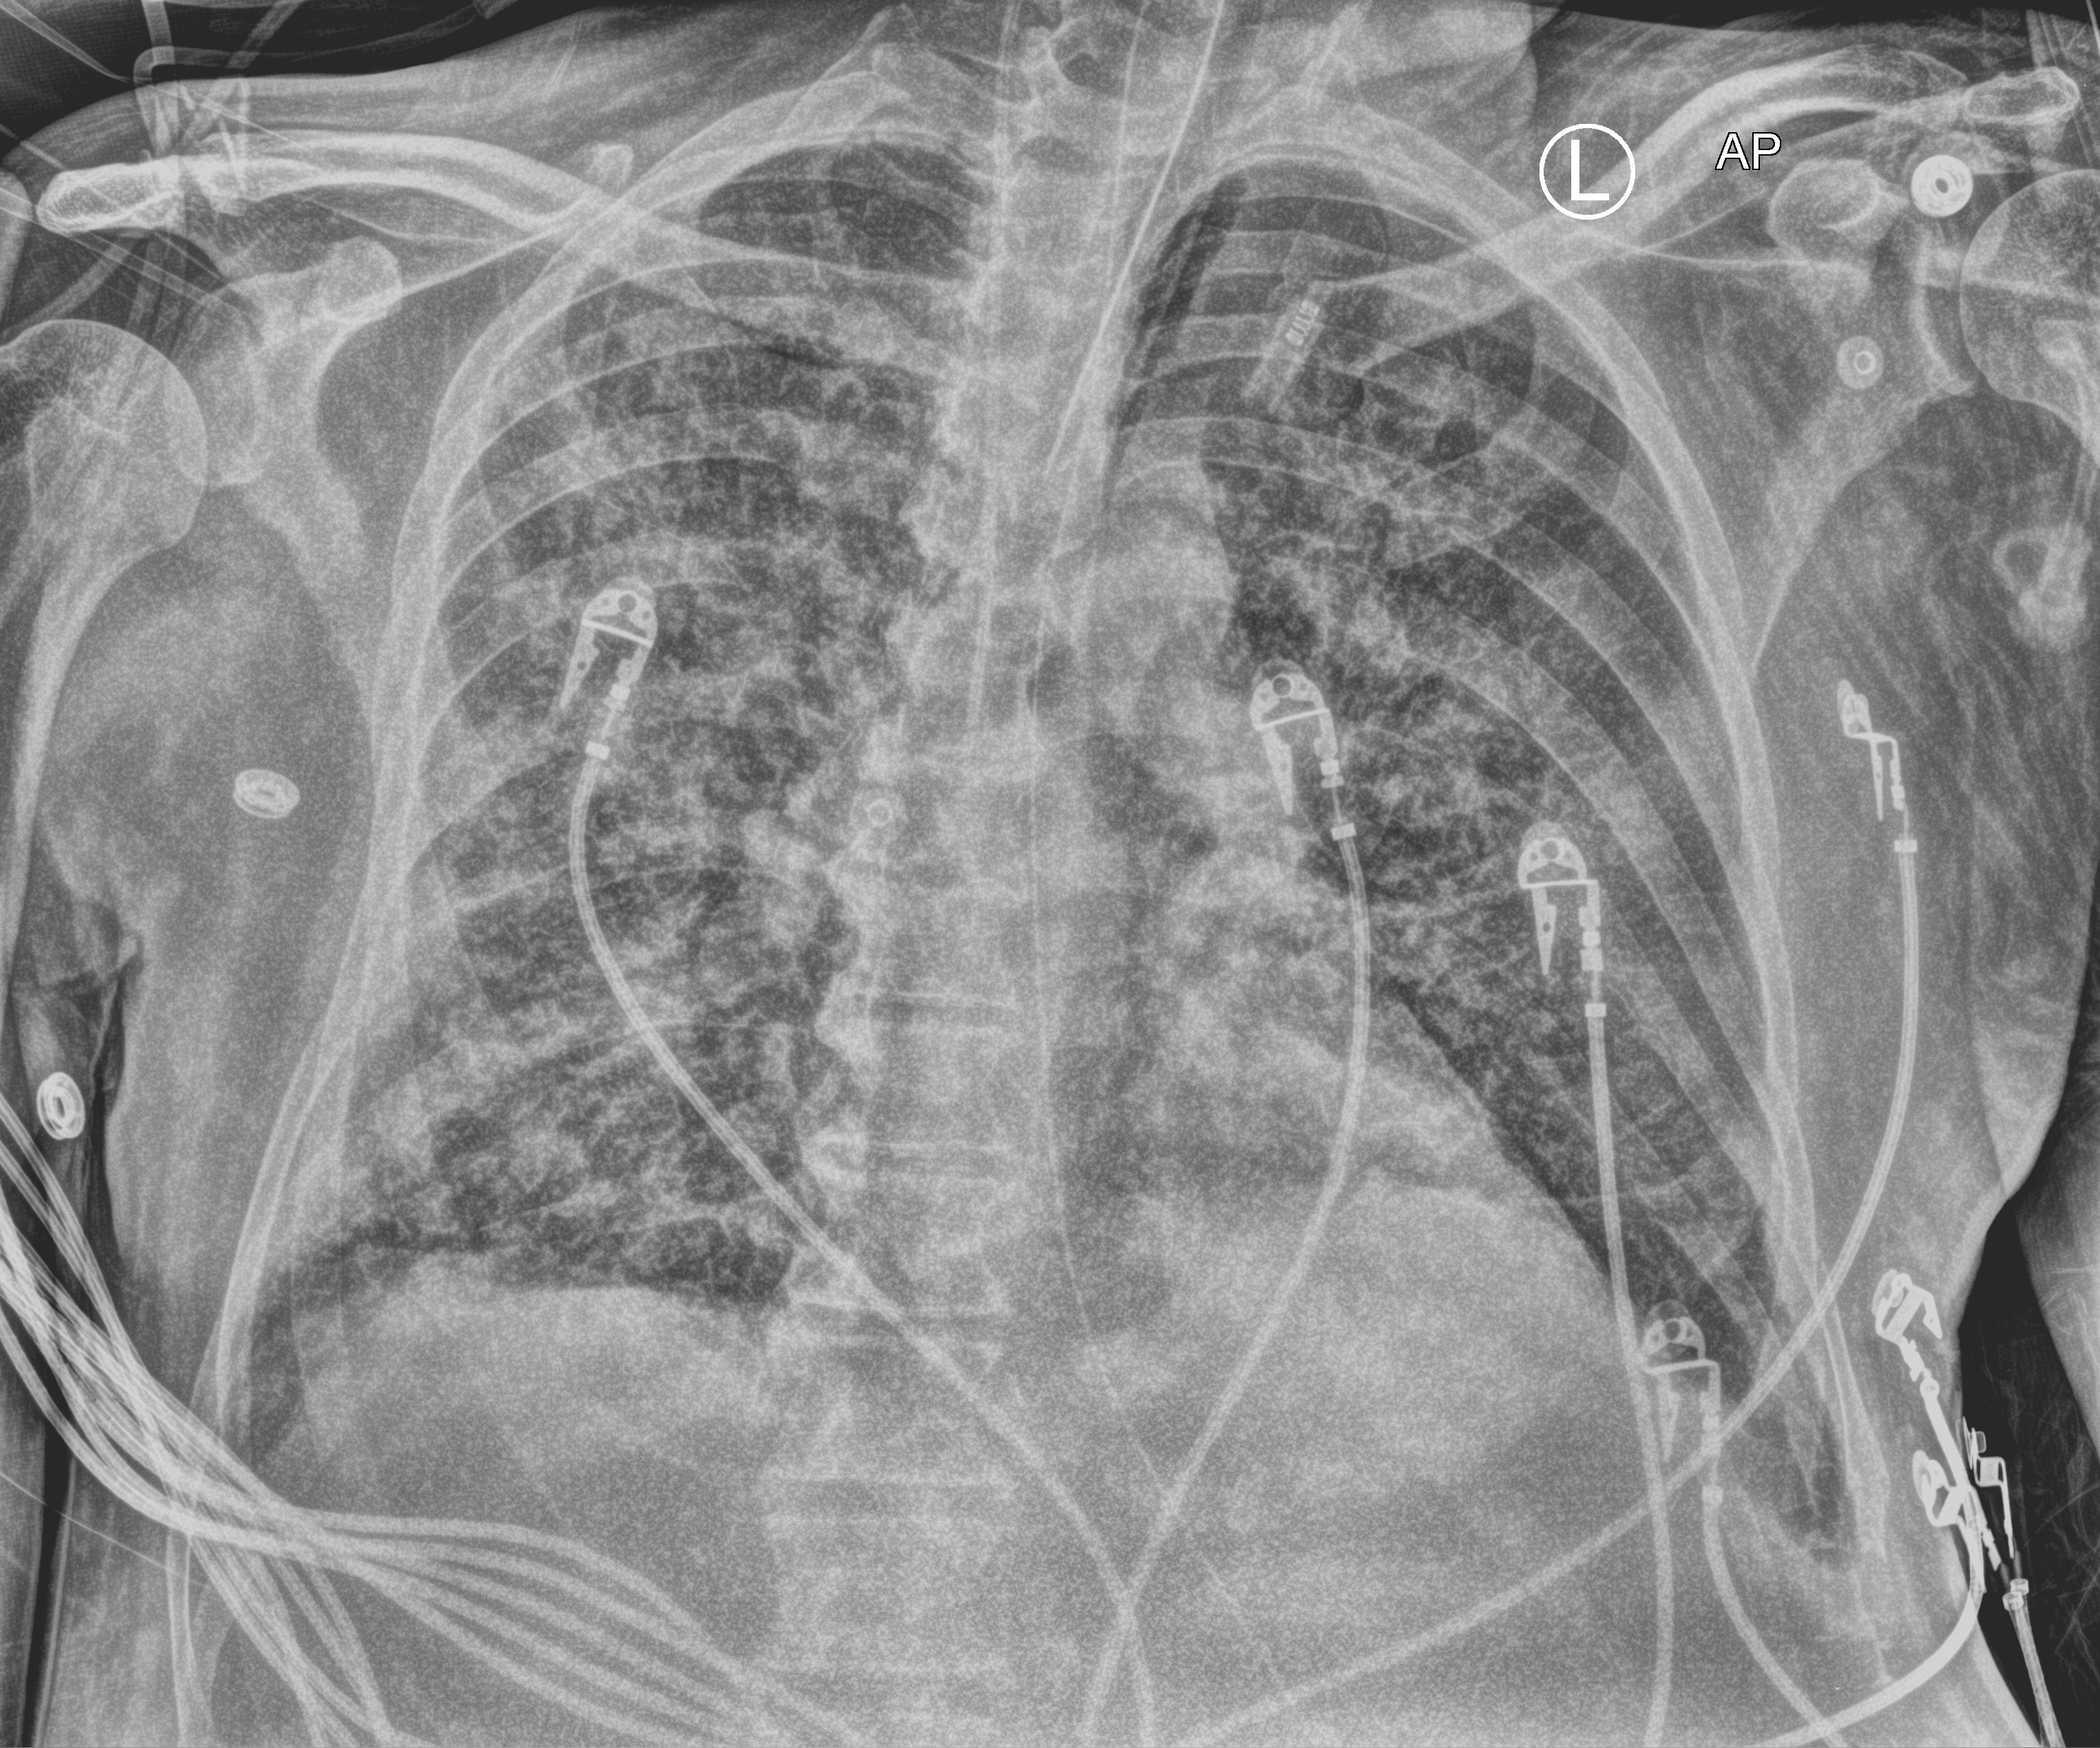
Bedside chest radiograph (computed radiography). Patient hospitalised with COVID-19; male, aged 60–74 years.
Admission-level facts for this patient (not findings on this image; timing relative to this image not recorded): length of hospital stay: 15 days.